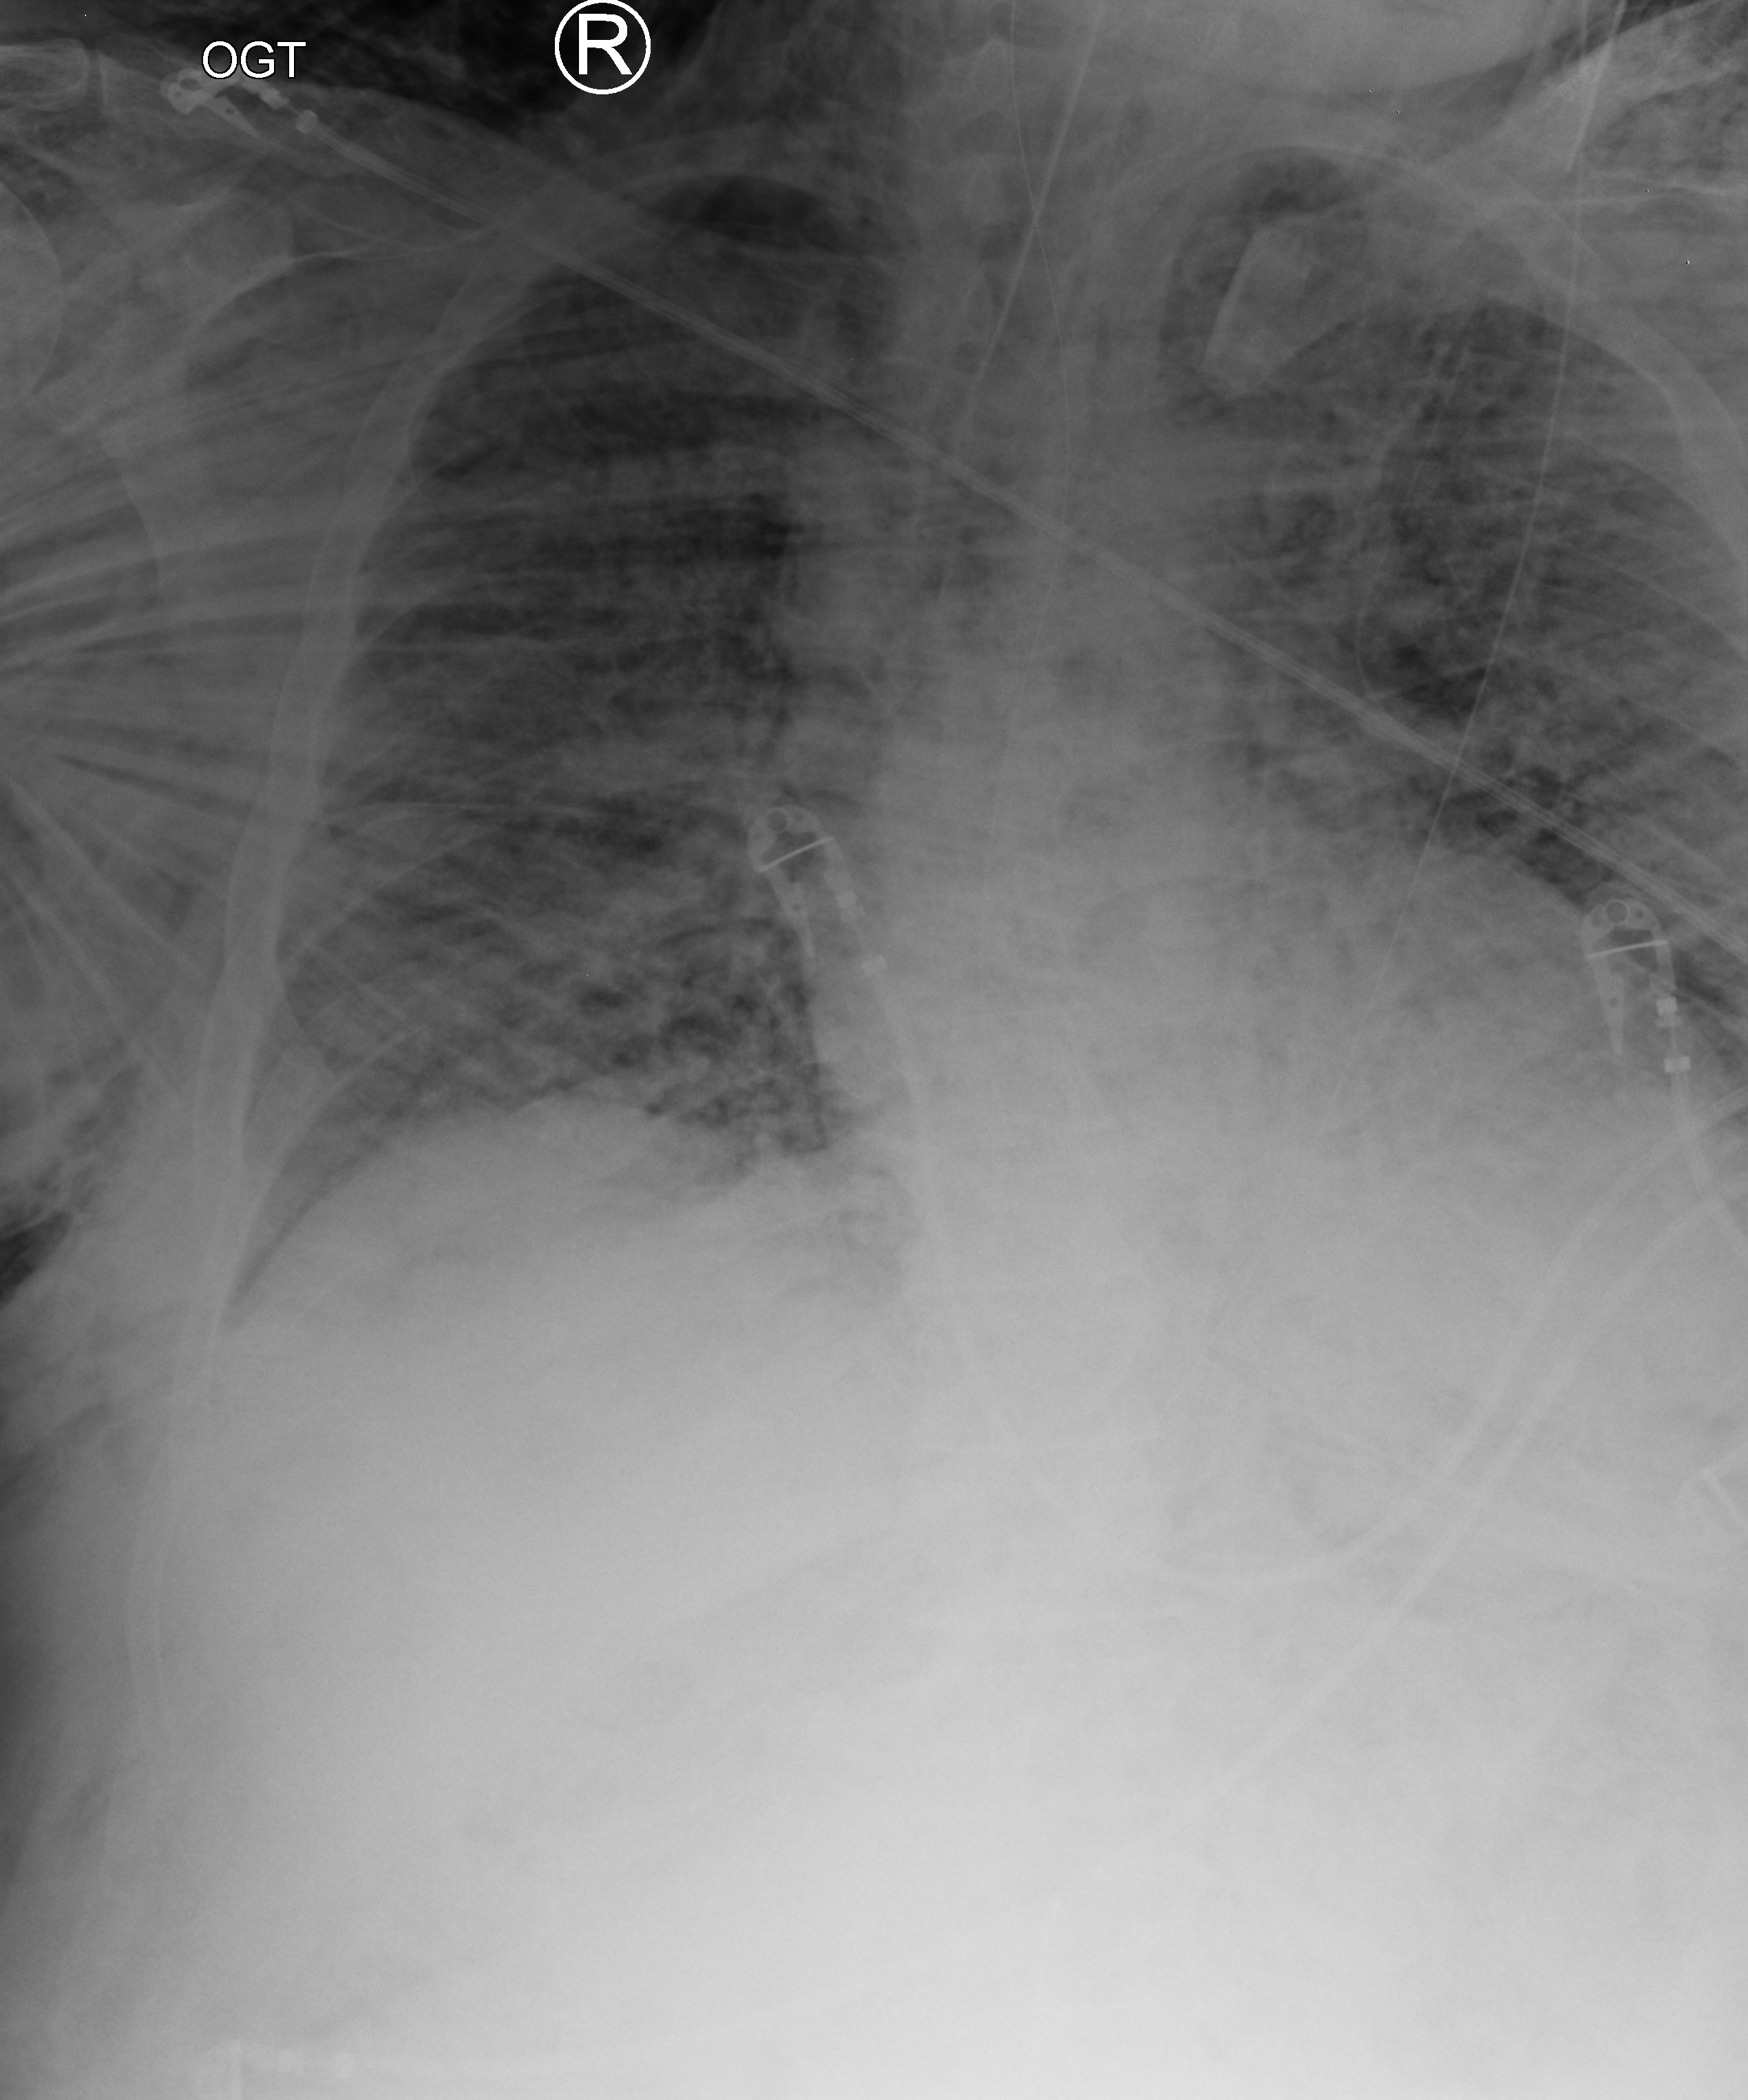
Bedside chest radiograph (computed radiography). Adult patient hospitalised with COVID-19, age 18–59 years.
Hospital-stay facts (about this admission, not read from this image; timing relative to this image not recorded): length of hospital stay: 26 days; admitted to intensive care during this hospital stay: yes.